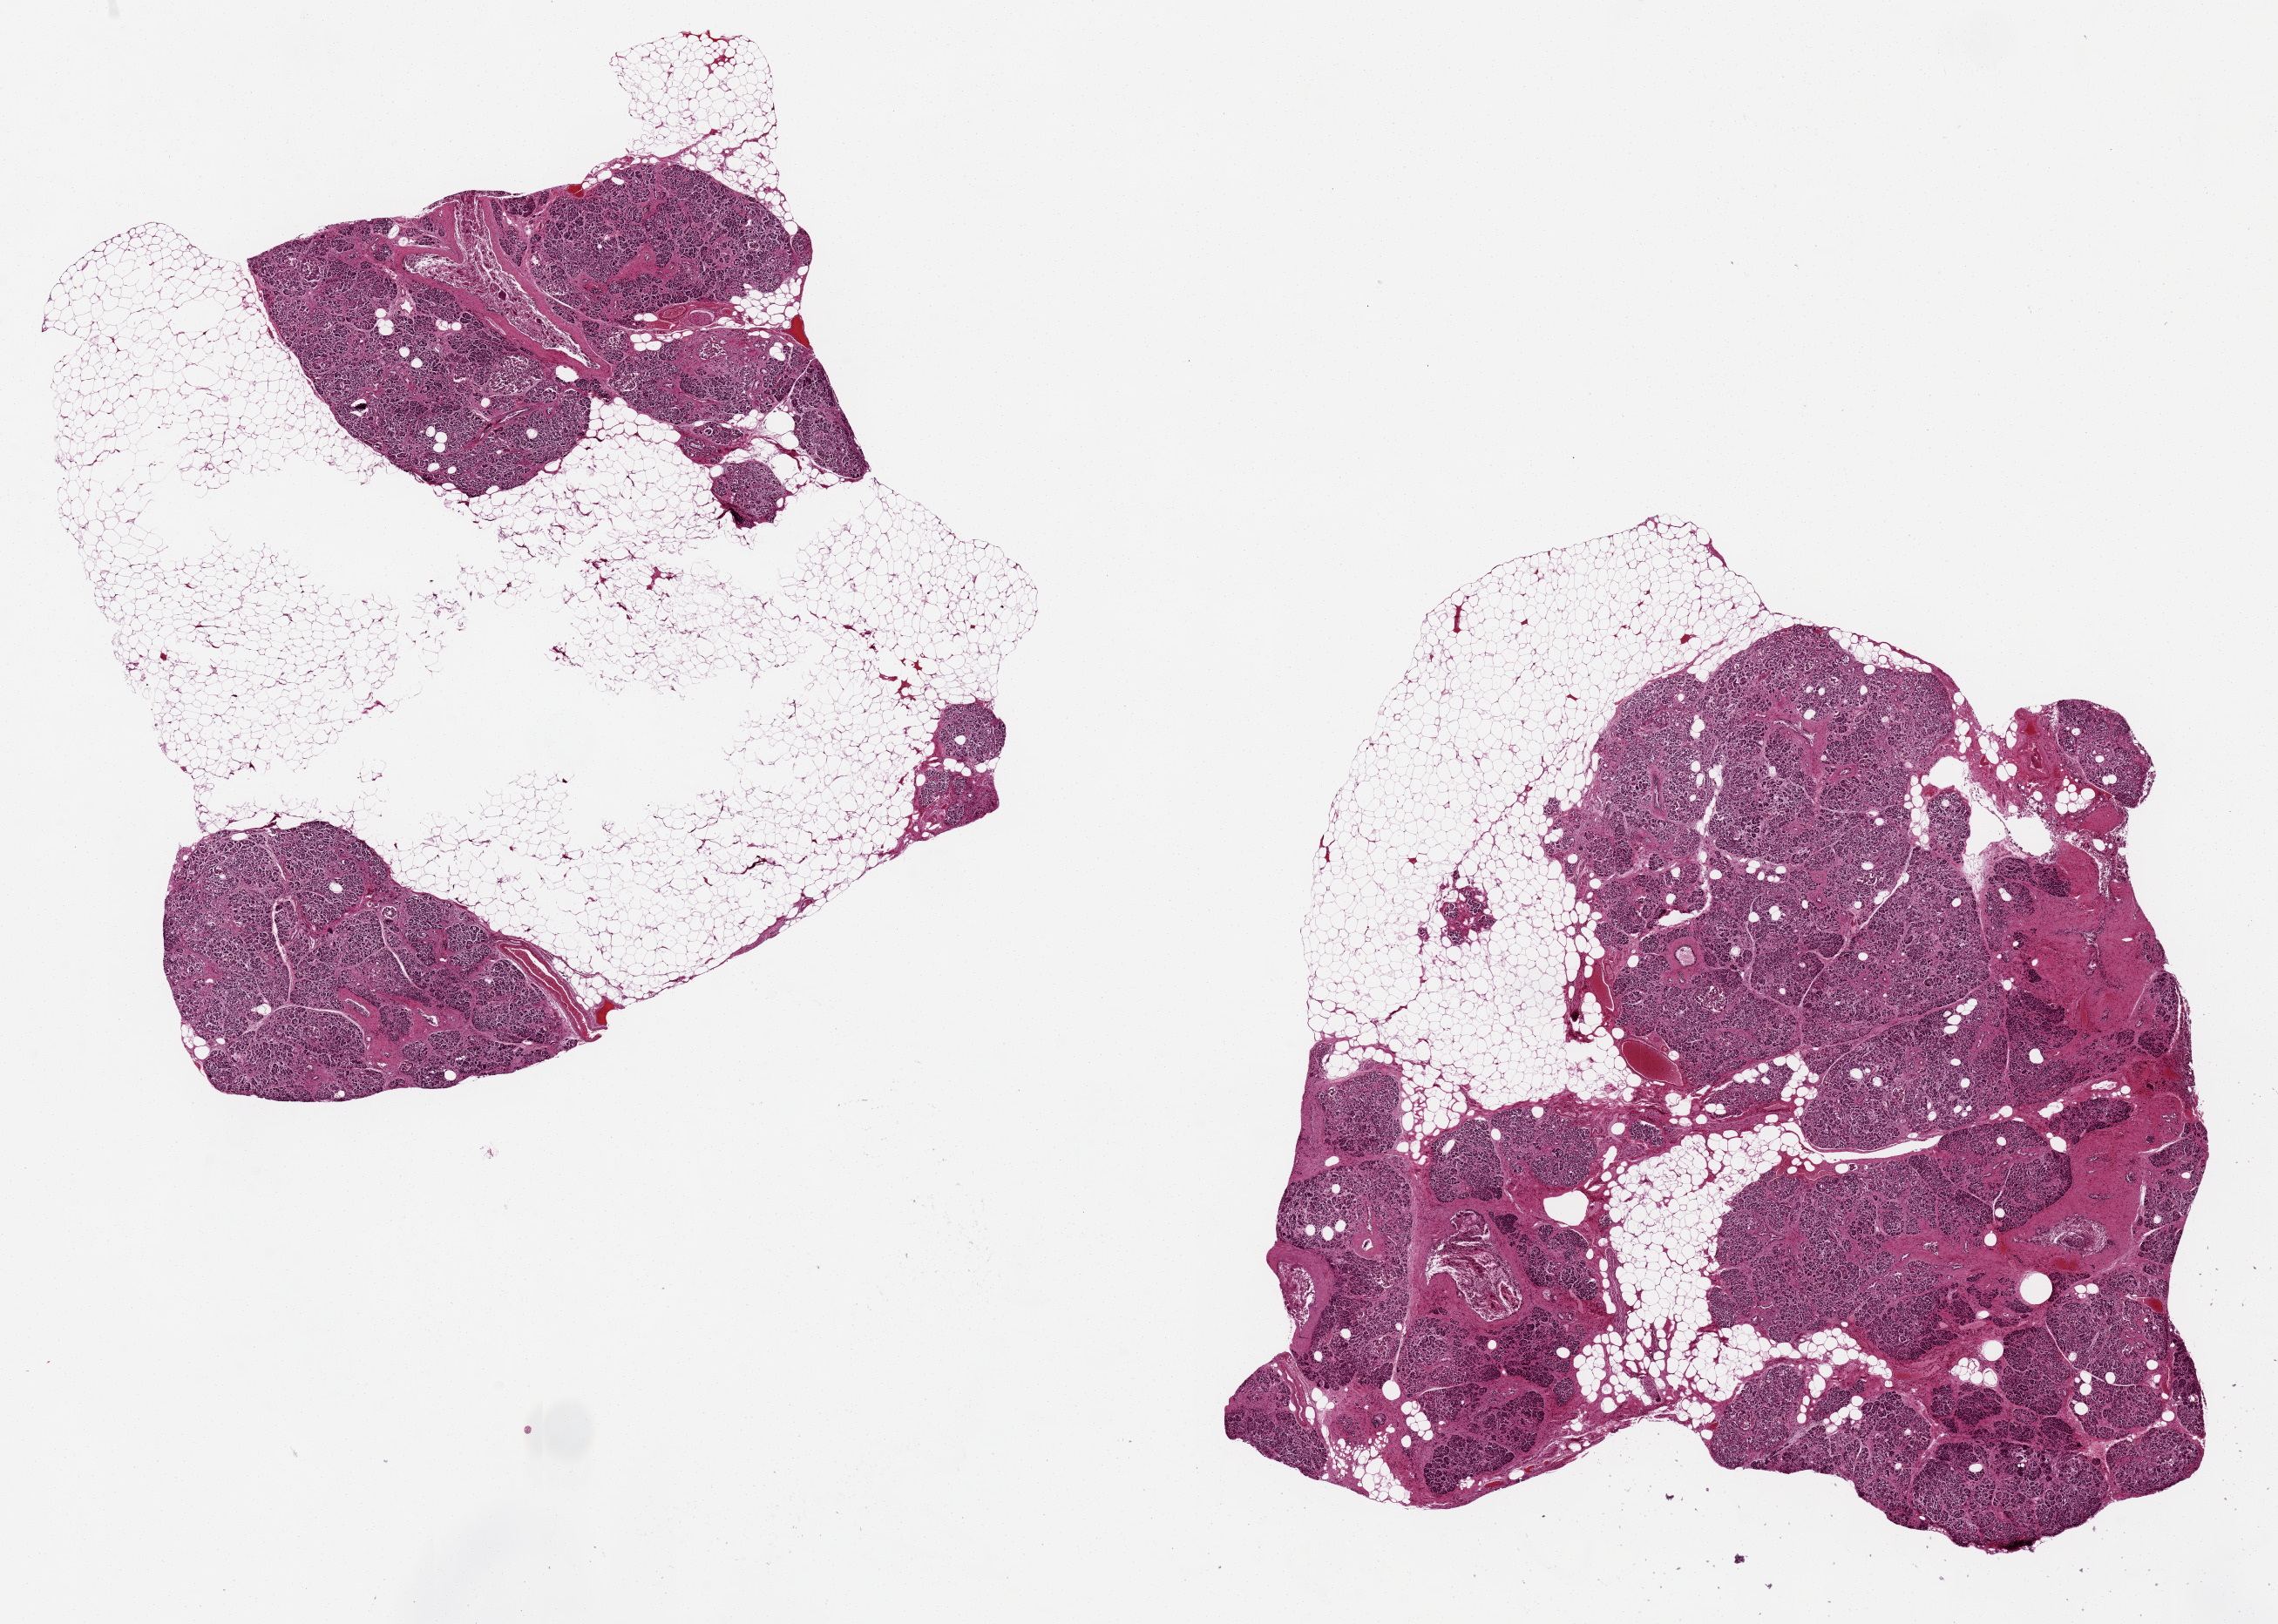
Digitized H&E-stained section, low-resolution overview of the scanned area, about 20.7 x 14.7 mm (acquisition: 20x scan). Donor: female.
Specimen: PAXgene-fixed paraffin-embedded (PFPE) section; target tissue: pancreas; tissue donor sample.